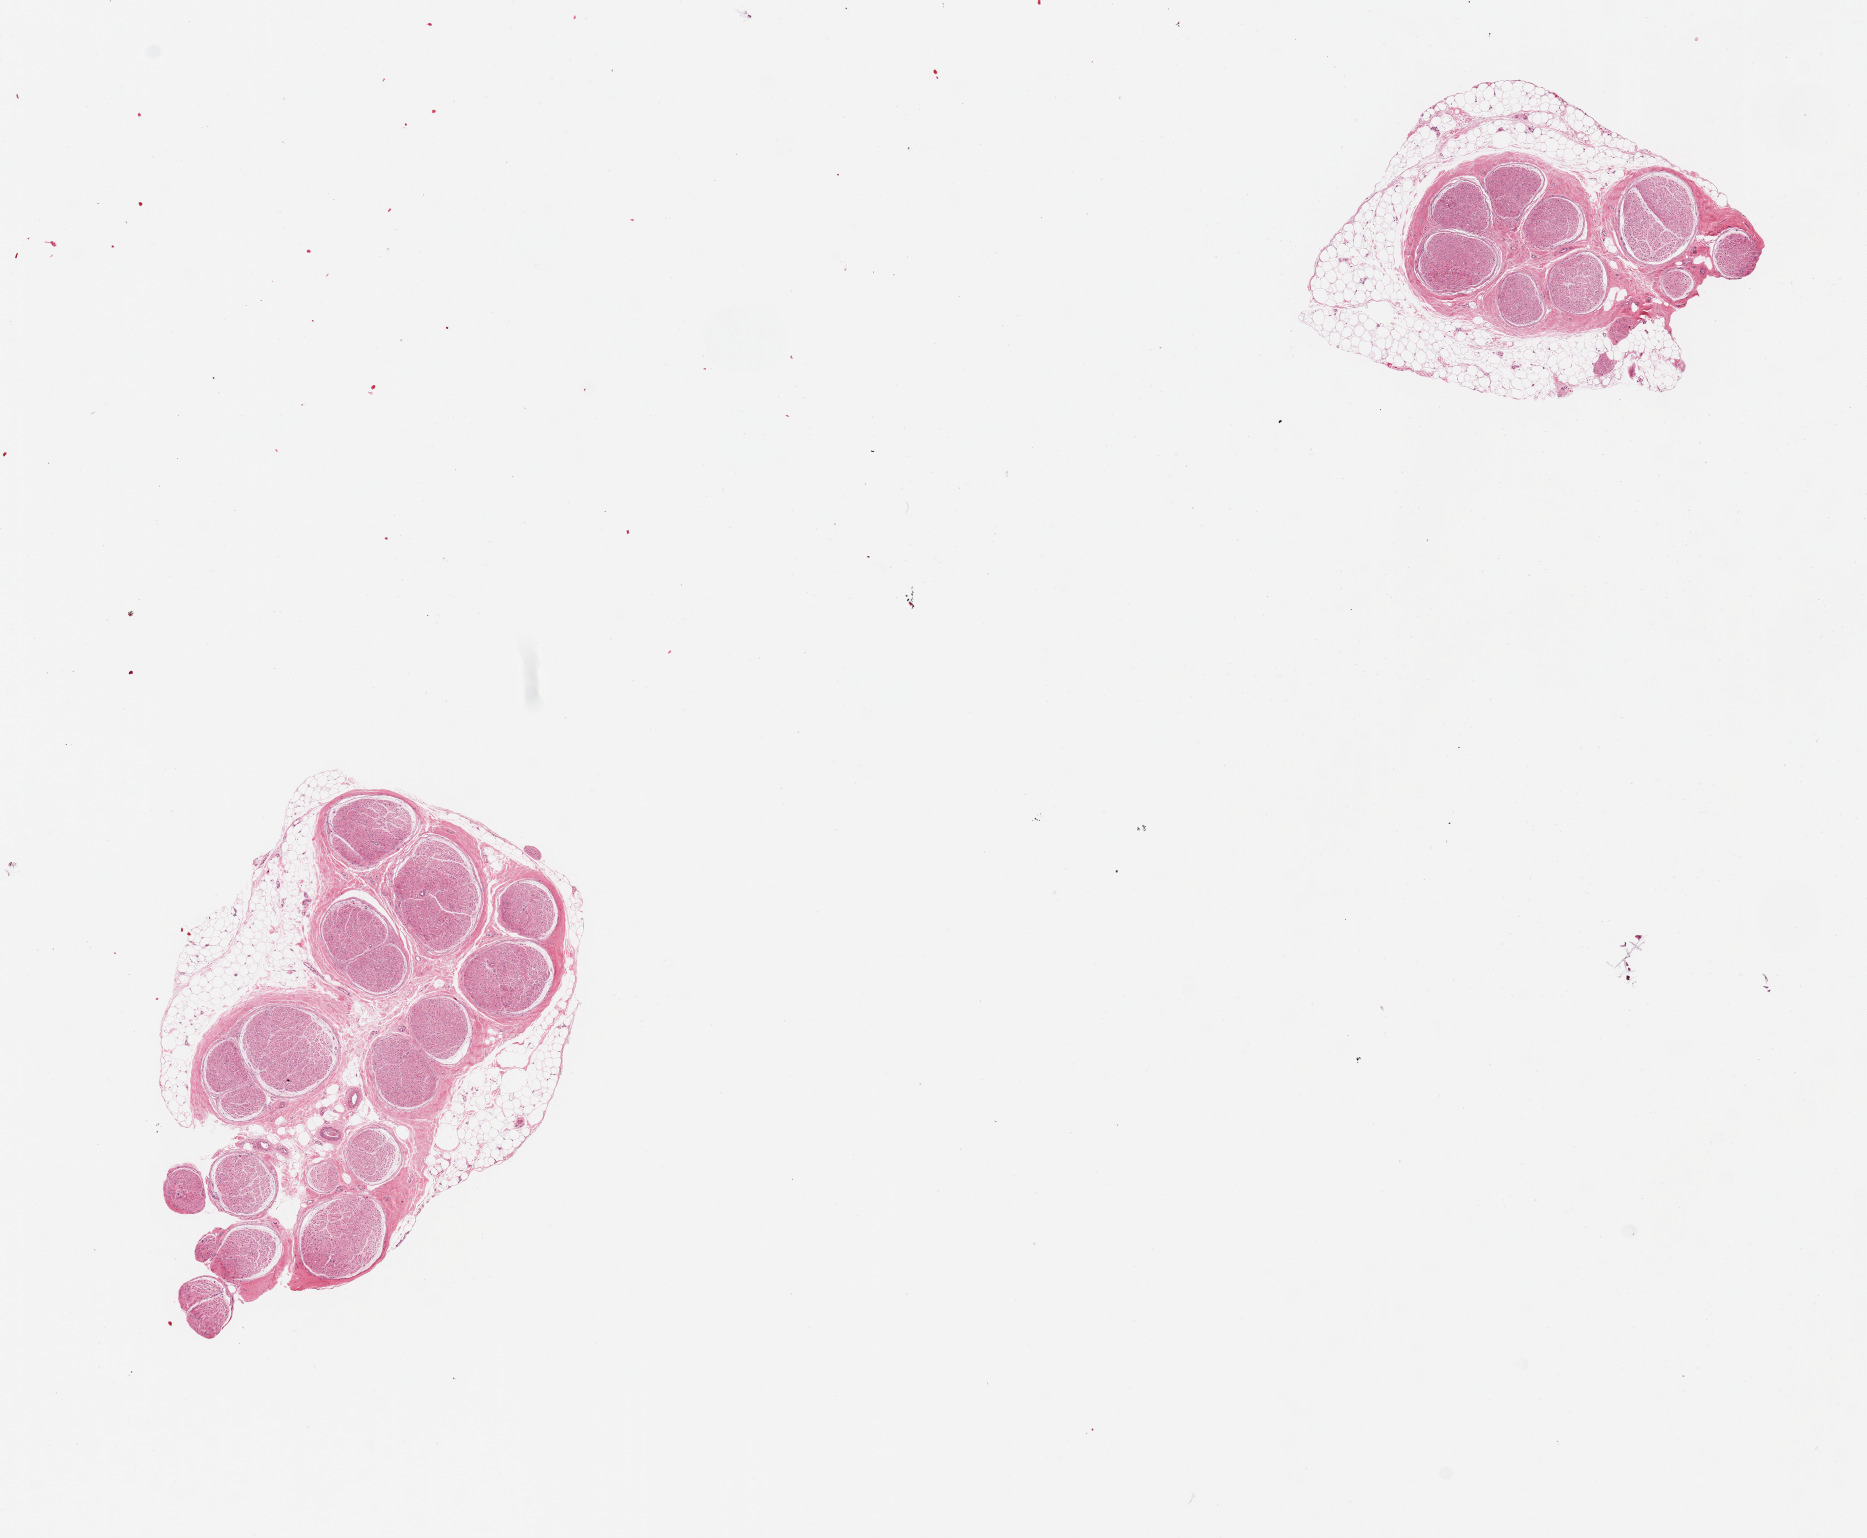
Whole-slide image, H&E stain, brightfield — shown as a low-resolution overview of the whole scanned area (about 14.8 x 12.2 mm, slide scanned at 20x), PAXgene-fixed, paraffin-embedded tissue, sampled site (target tissue): tibial nerve, tissue donor sample.
Review note (as recorded): 2 pieces, discontinous rim of adherent fat, ~0.5-1 mm.